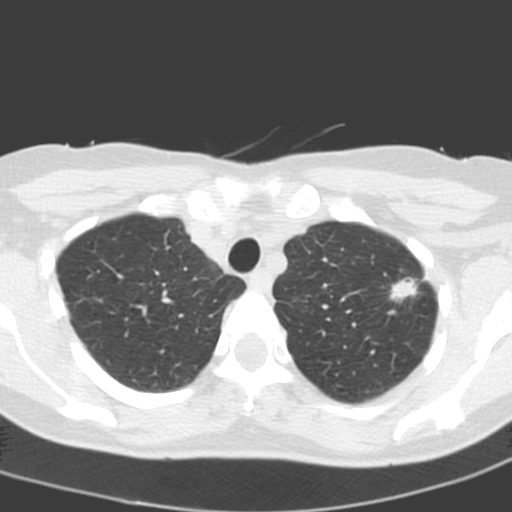
Chest CT (low-dose screening protocol), one axial image; first (baseline) screen; lung window (W 1500 / L -600 HU); slice 35 of 193 in the series; 512 × 512 image matrix, field of view 272 × 272 mm. Female participant, aged 58 years at enrolment.
• Expert reader's lesion annotation, bounding box <379,268,427,317> (left, top, right, bottom; pixels).
• Screening reader's record for this exam (one nodule recorded; not confirmed to be the boxed lesion): non-calcified nodule or mass ≥4 mm, left upper lobe, 14 × 10 mm, spiculated (stellate) margins, soft tissue attenuation.
• Later outcome: lung cancer diagnosed 48 days after this screen — adenocarcinoma, NOS, left upper lobe, poorly differentiated (G3), stage IA (AJCC 6th edition), 13 mm at pathology.